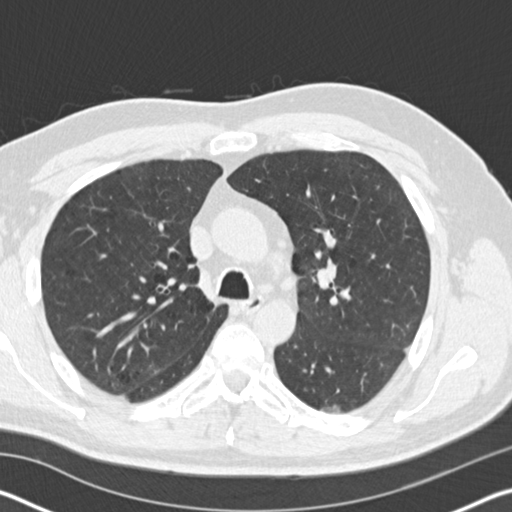
Low-dose screening chest CT, one axial slice. Slice 117 of 178 in the series (ordered by position). 120 kVp. Lung window (W 1500 / L -600 HU). 2 mm slice thickness. 512 × 512 image matrix, field of view 340 × 340 mm.
Structures marked on this image (expert manual segmentation):
- lesion 1 (tumor, lower lobe of left lung): bounding box [x1, y1, x2, y2] px = [322, 406, 341, 414]